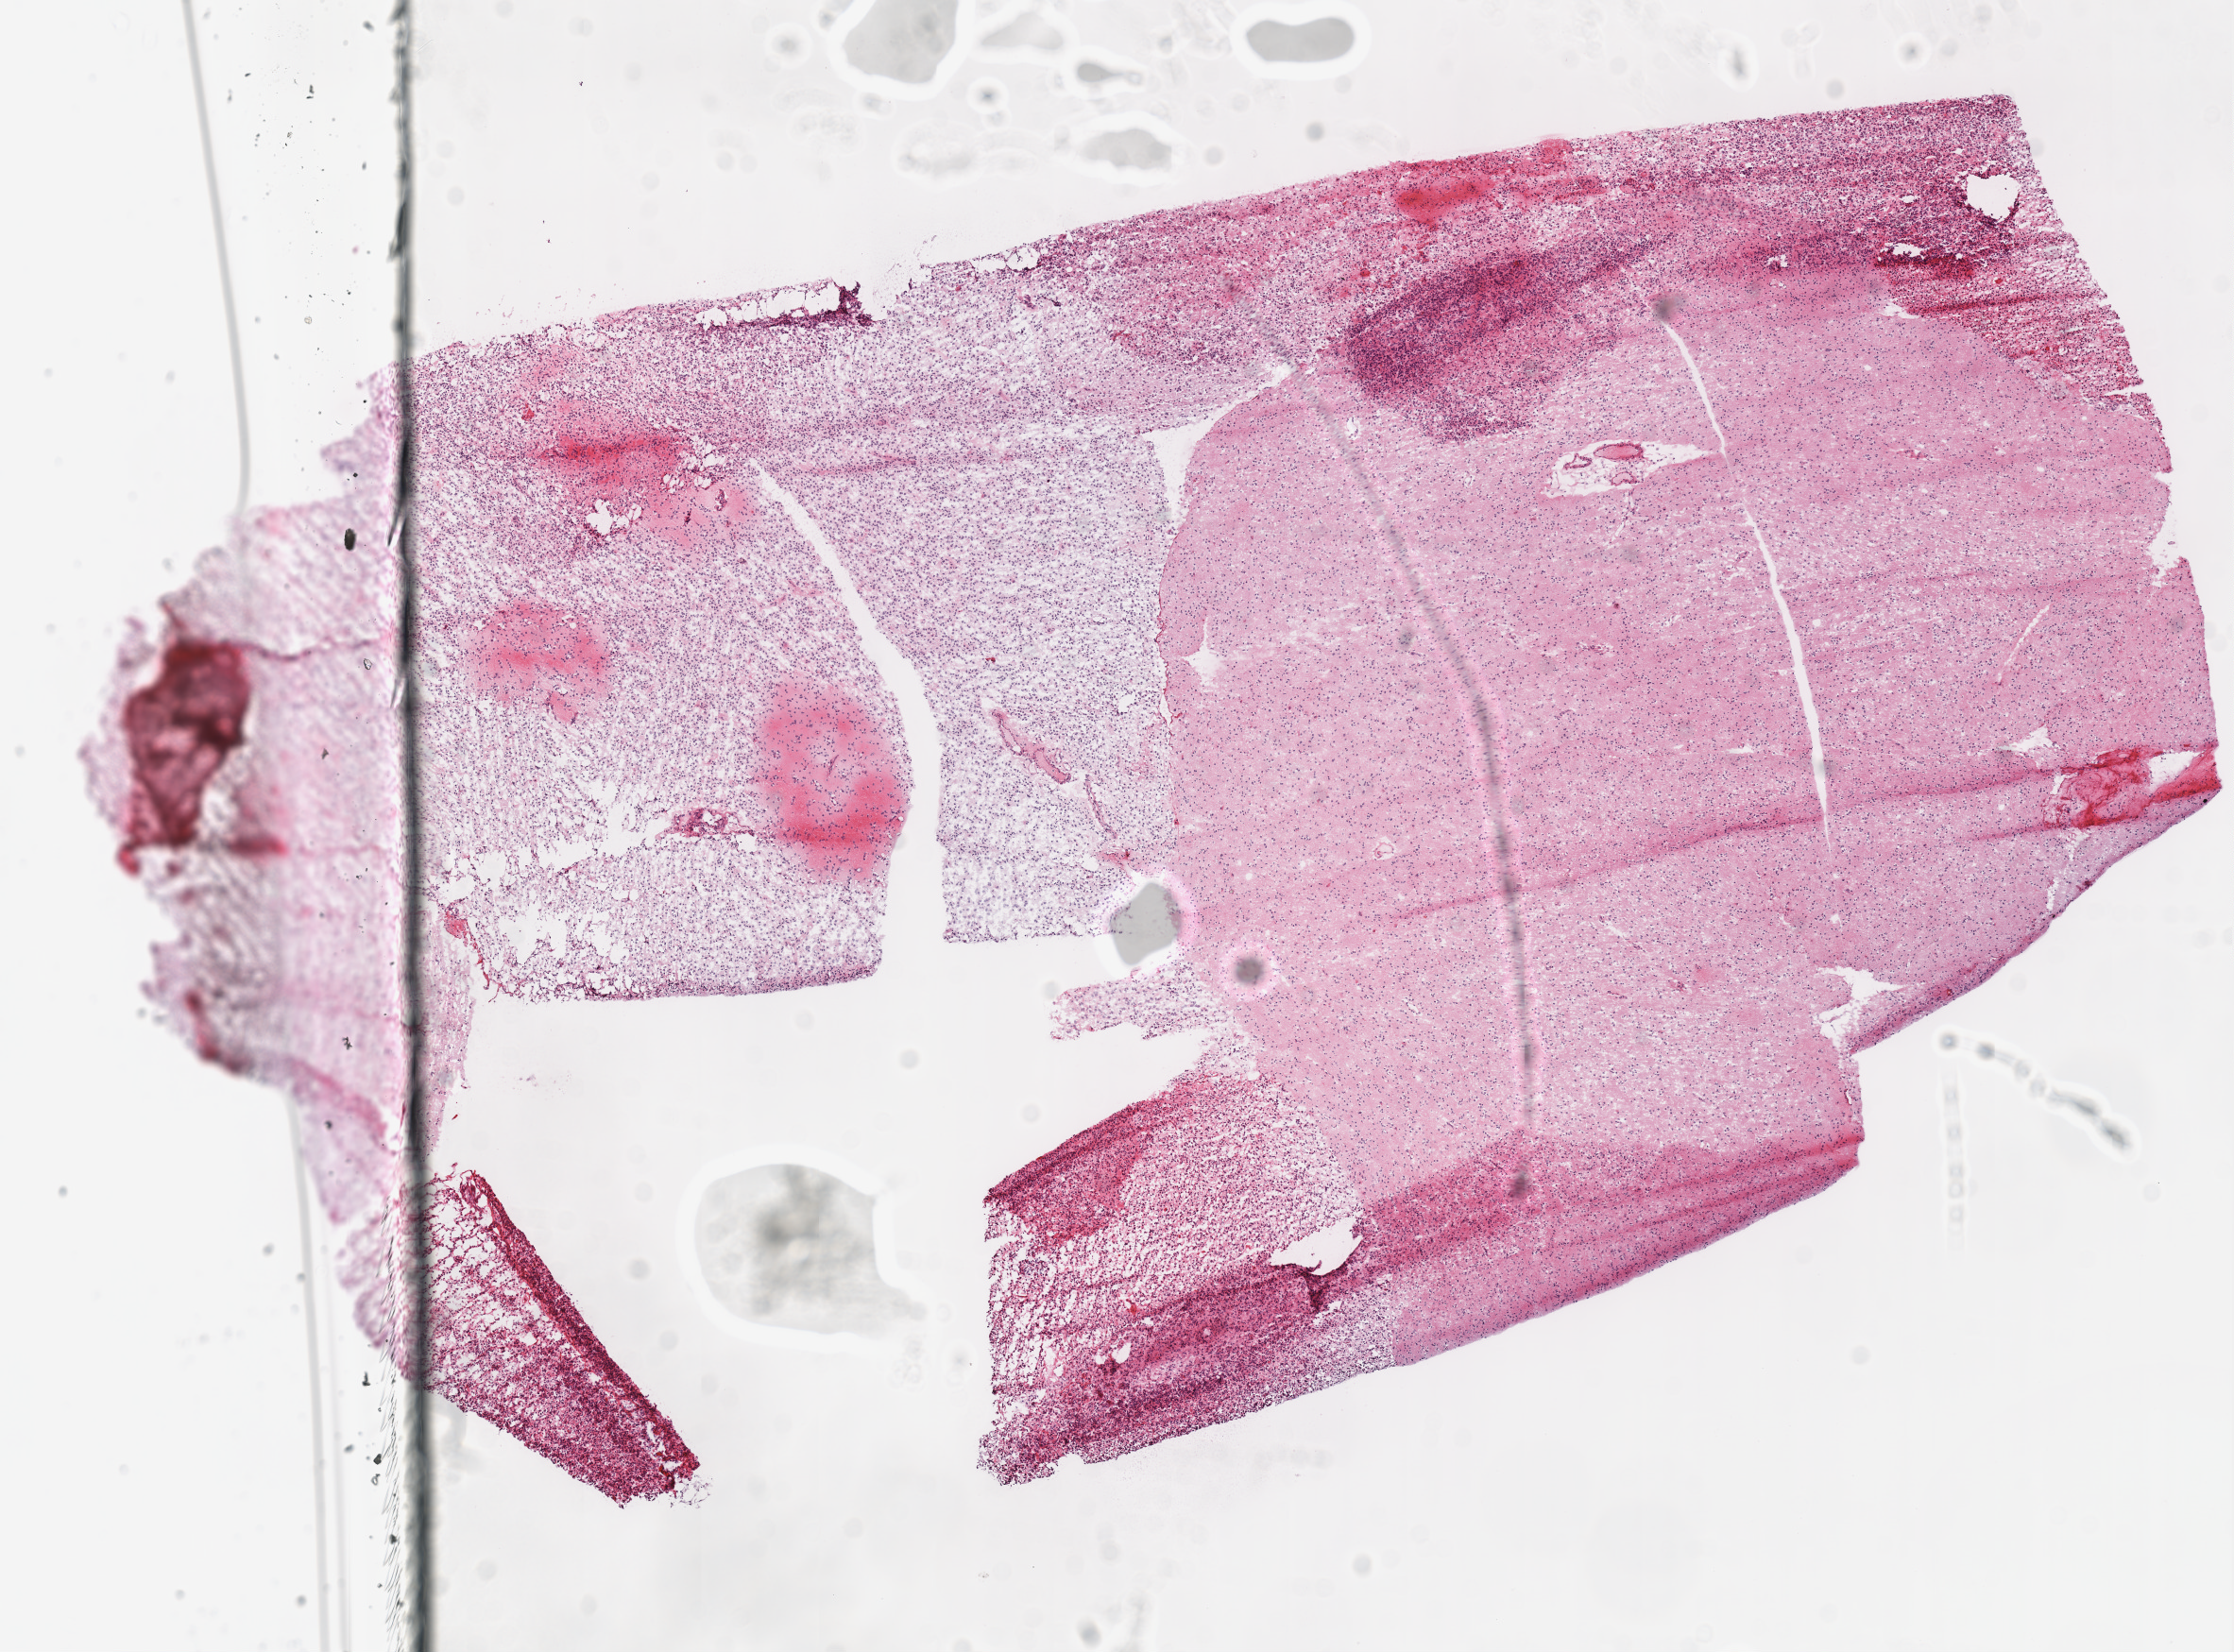
H&E-stained whole-slide image, a low-resolution overview of the entire scanned area, about 9.3 x 6.9 mm; frozen section from the top of the tissue portion; primary tumour sample from the brain. Male, age 39 years at initial diagnosis. Histologic grade: G2 (moderately differentiated). Pathologist review of this section (percent, as recorded): tumour cells 100%, tumour nuclei 80%, normal cells 0%, stromal cells 0%, necrosis 0%.
* pathologic diagnosis: Oligodendroglioma, NOS (cerebrum)
* laterality: left